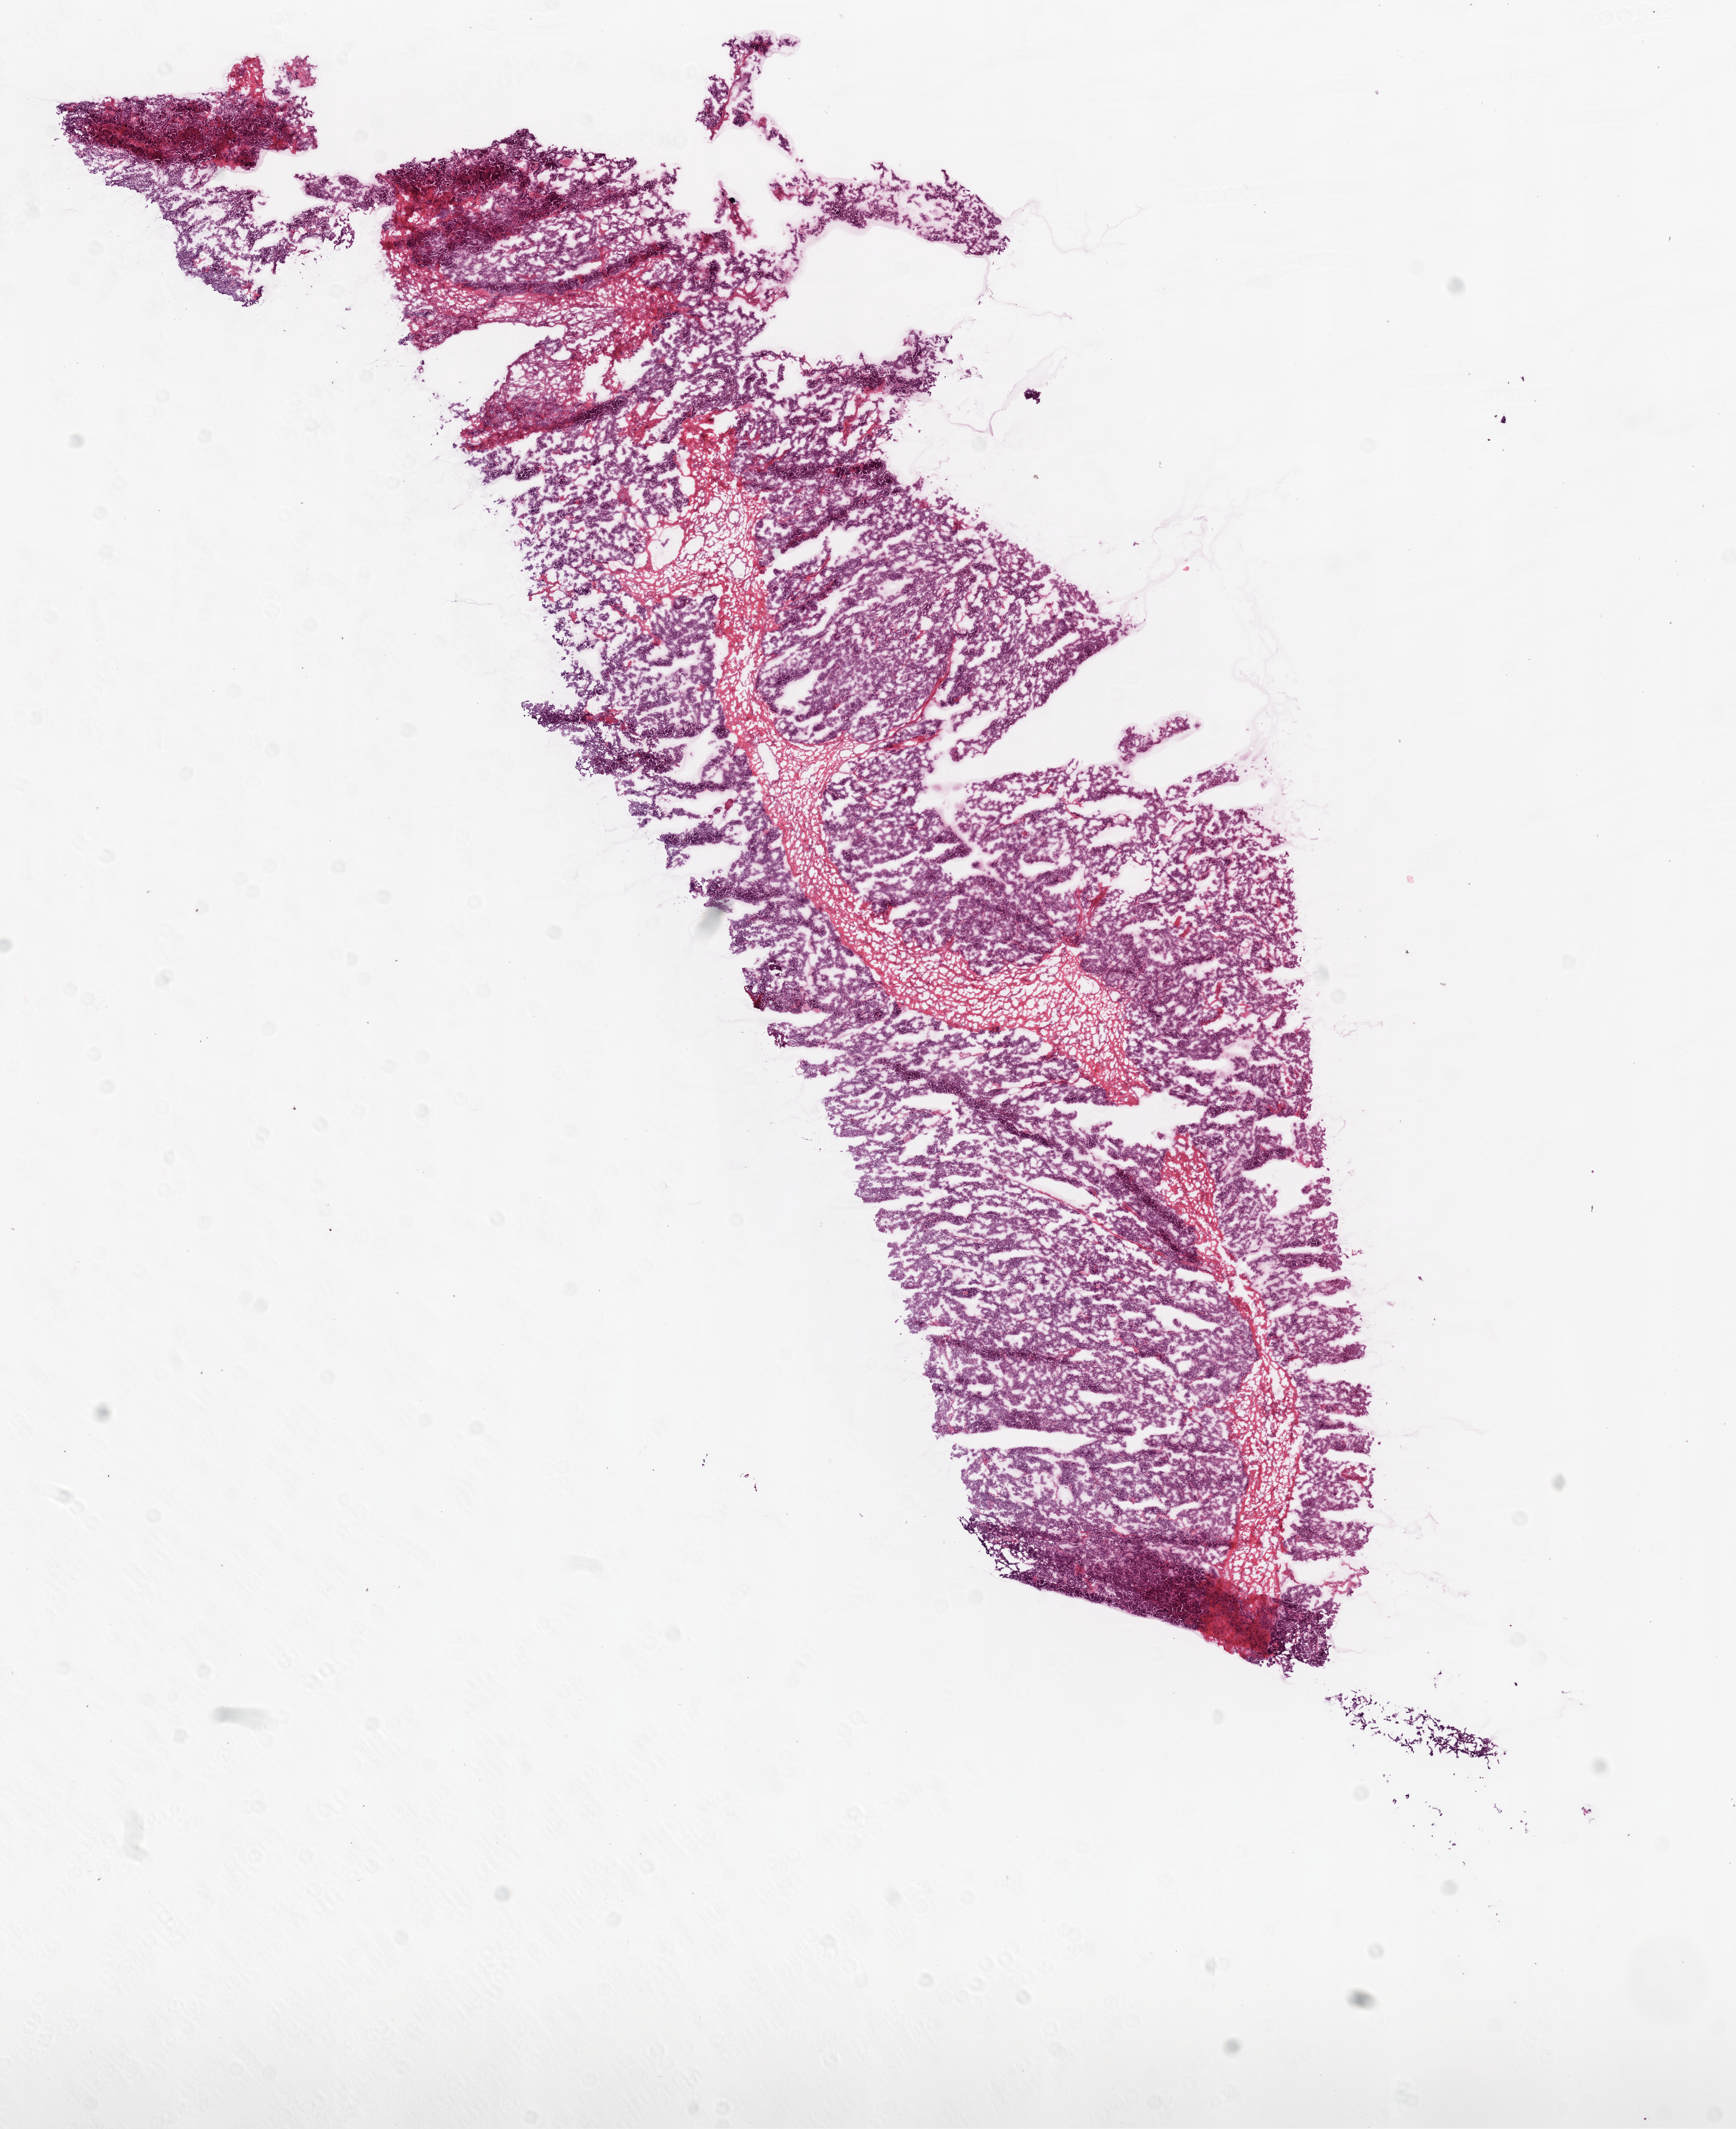
Whole-slide histology image, H&E-stained — shown as a low-resolution overview of the whole scanned area (about 10.0 x 12.3 mm). Frozen section from the bottom of the tissue portion. Sample: primary tumour, ovary. Female patient; age at initial diagnosis 49 years. Histologic grade: G2 (moderately differentiated). Slide review estimates, as recorded: tumour cells 90%, tumour nuclei 95%, normal cells 0%, stromal cells 10%, necrosis 0%.
- histologic diagnosis: Serous cystadenocarcinoma, NOS
- FIGO stage: IIIB
- laterality: bilateral